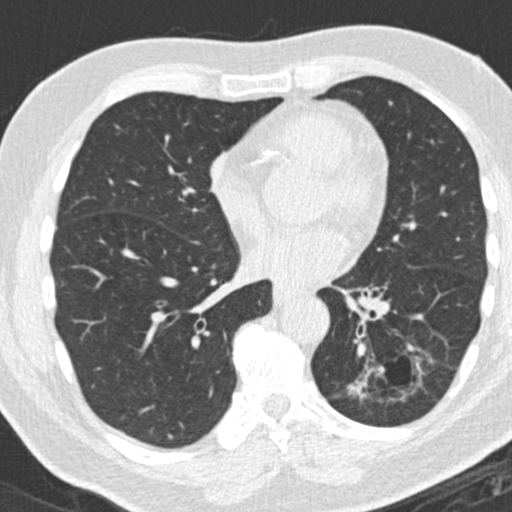
Axial slice from a low-dose chest CT screening exam; third annual screen; lung window (W 1500 / L -600 HU); 2 mm slice thickness; 120 kVp; slice 95 of 180 in the series. Male, age 66 years at enrolment. Former smoker at enrolment.
• Expert reader's lesion annotation, bounding box <355,345,426,428> (left, top, right, bottom; pixels).
• Reader record for this screening exam (exam-level; its link to the box is not recorded): non-calcified nodule or mass ≥4 mm, left lower lobe, 31 × 24 mm, spiculated (stellate) margins, pre-existing on the prior screen: yes; interval growth: yes.
• Official screen result: positive, other.
• Lung cancer was diagnosed 56 days after this screen: adenocarcinoma, NOS, left lower lobe, poorly differentiated (G3), stage IB (AJCC 6th edition), 38 mm at pathology.